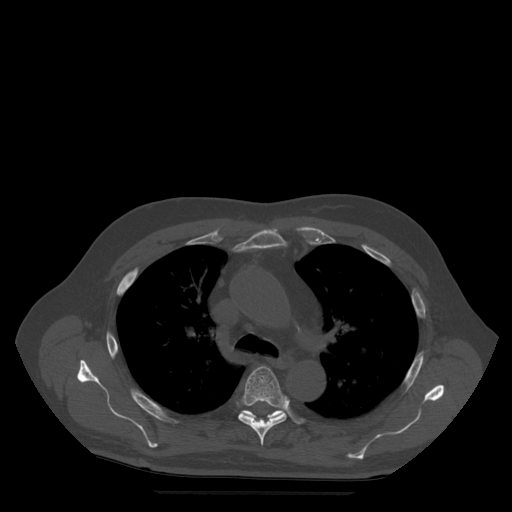
CT including the spine, one axial slice; slice 369 of 522 in the series (ordered by position); bone window (W 1800 / L 400 HU); 1.25 mm slice thickness; 512 × 512 image matrix, field of view 420 × 420 mm. Patient age 72 years. From the clinical record (not read from this slice): primary cancer: prostate.
Annotated regions visible in this slice (semi-automatically segmented with operator editing):
- T5 vertebra: bounding box <238,367,290,446> (left, top, right, bottom; pixels)
- T6 vertebra: <243,410,301,431>